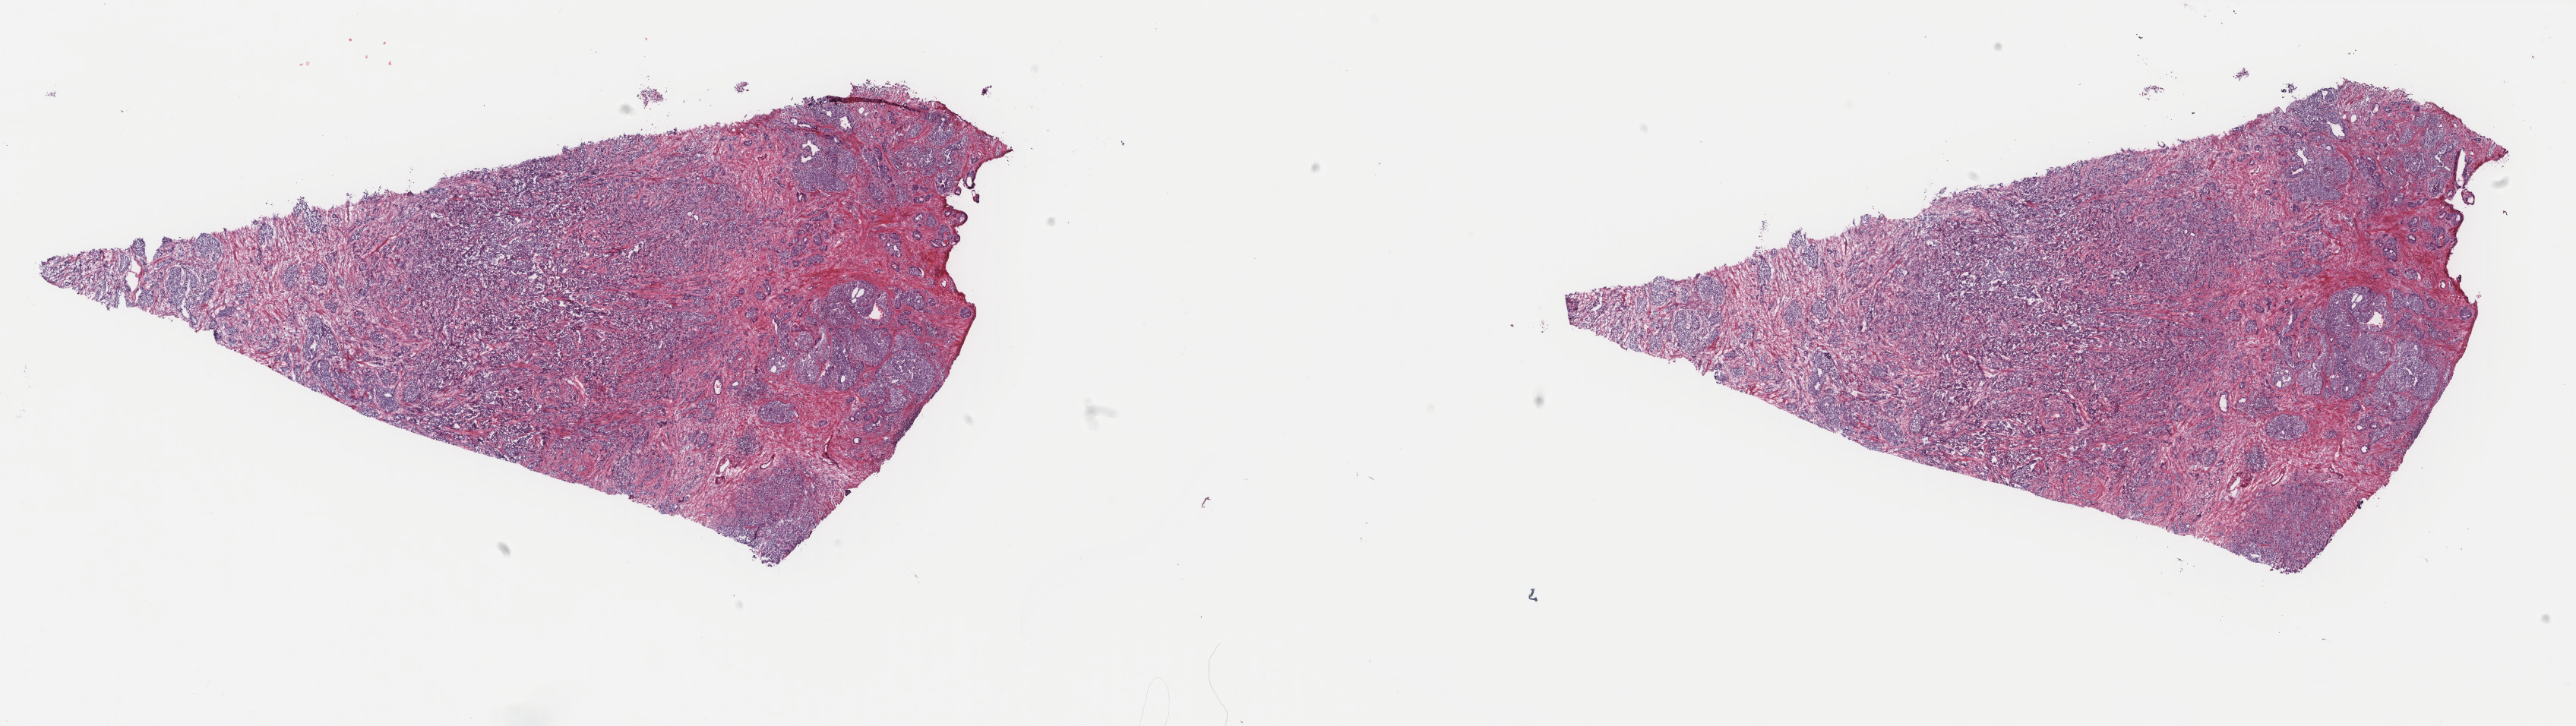
Digitized H&E tissue section (whole slide), a low-resolution overview of the entire scanned area, about 26.9 x 7.6 mm, frozen section from the top of the tissue portion, sample: primary tumour, prostate. Male, age 64 years at initial diagnosis. Gleason score: 9 (4+5). Slide review estimates, as recorded: tumour cells 73%, tumour nuclei 90%, normal cells 0%, stromal cells 25%, necrosis 2%. Inflammatory infiltration, as recorded: lymphocyte infiltration 5%, monocyte infiltration 0%, neutrophil infiltration 0%.
Pathologic diagnosis: Adenocarcinoma, NOS (prostate gland). Laterality: bilateral. Lymph nodes positive (case pathology): 8 of 20 examined.